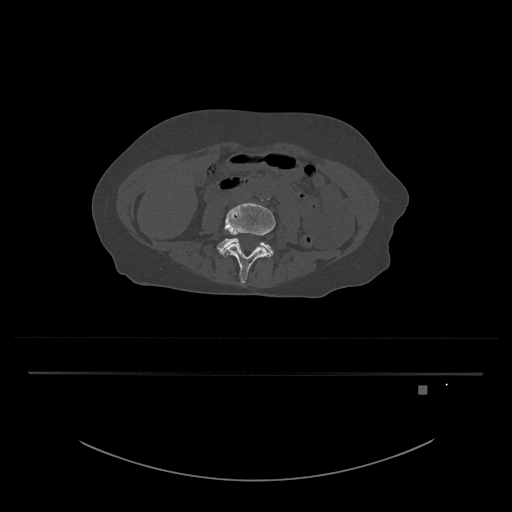
CT including the spine, one axial slice. Position 347 of 797 along the scan axis. Reconstruction kernel Br40s/3. Bone window (W 1800 / L 400 HU). 512 × 512 image matrix, field of view 500 × 500 mm. Female patient, age 57 years. Case-level facts recorded for this patient, not image findings: primary cancer: cervical.
Outlined on this slice (semi-automatically segmented with operator editing):
- L4 vertebra: box from (x=220, y=203) to (x=276, y=284) px